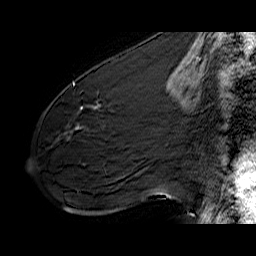
Breast MRI (dynamic contrast-enhanced), one sagittal slice. Position 33 of 60 along the scan axis. Dynamic contrast-enhanced series, time point 2 of 6 at this slice position (early post-contrast). 1.5 T. TE 6.4 ms, TR 32.9 ms. 4 mm slice thickness. 256 × 256 image matrix. Female patient. From the clinical record (not read from this slice): setting: breast cancer imaged before/during neoadjuvant chemotherapy; receptor status: HER2-positive.
Annotated regions visible in this slice (semi-automatically segmented with operator editing):
- analysis volume of interest (the breast-tissue region the enhancement analysis was run in; not a lesion): bounding box <61,77,141,142> (left, top, right, bottom; pixels)
- tumour enhancement mask (voxels above the 100 % enhancement threshold inside the analysis volume of interest): <73,83,100,110>